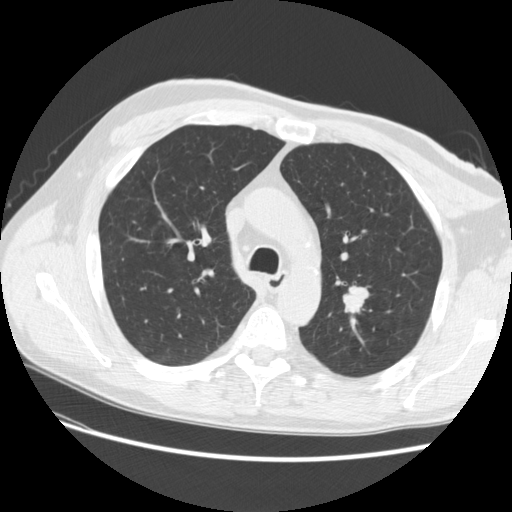
Low-dose screening chest CT, one axial slice; position 182 of 256 along the scan axis; lung window (W 1500 / L -600 HU); 512 × 512 image matrix, field of view 366 × 366 mm.
Structures marked on this image (outlined manually by an expert reader):
- lesion 1 (tumor, upper lobe of left lung): bounding box <343,287,368,313> (left, top, right, bottom; pixels)